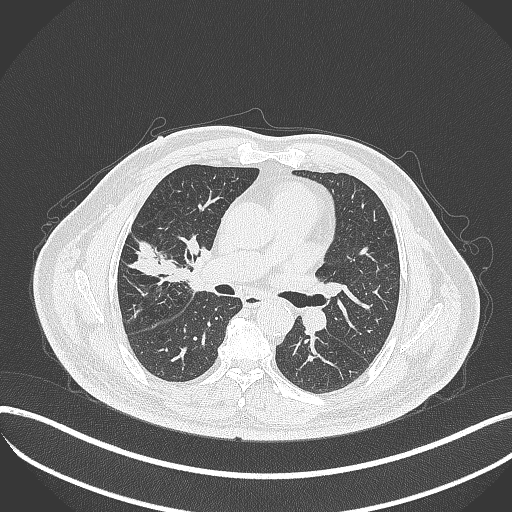
Chest CT, one axial slice. Position 203 of 401 along the scan axis. 120 kVp. Lung window (W 1500 / L -600 HU). 1 mm slice thickness. 512 × 512 image matrix. Patient: male, 72 years. Case-level facts recorded for this patient, not image findings: clinical TNM (as recorded): T1c N0 M0.
Outlined on this slice (rectangle marked by the reading radiologist):
- lung tumour (recorded histology: squamous cell carcinoma): bounding box (x1, y1, x2, y2) in pixels: (179, 231, 211, 297)